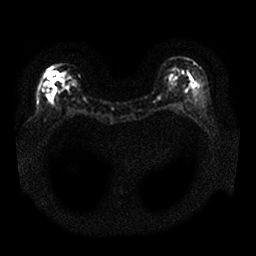
Breast MRI, one axial slice; position 9 of 25 along the scan axis; diffusion-weighted series; image 2 of 4 stored at this slice position (different b-values; order by instance number); 1.5 T; 4 mm slice thickness; 256 × 256 image matrix, field of view 340 × 340 mm. Female patient.
Annotated regions visible in this slice (outlined manually by an expert reader):
- tumour on diffusion-weighted imaging: bounding box [x1, y1, x2, y2] px = [46, 70, 63, 85]